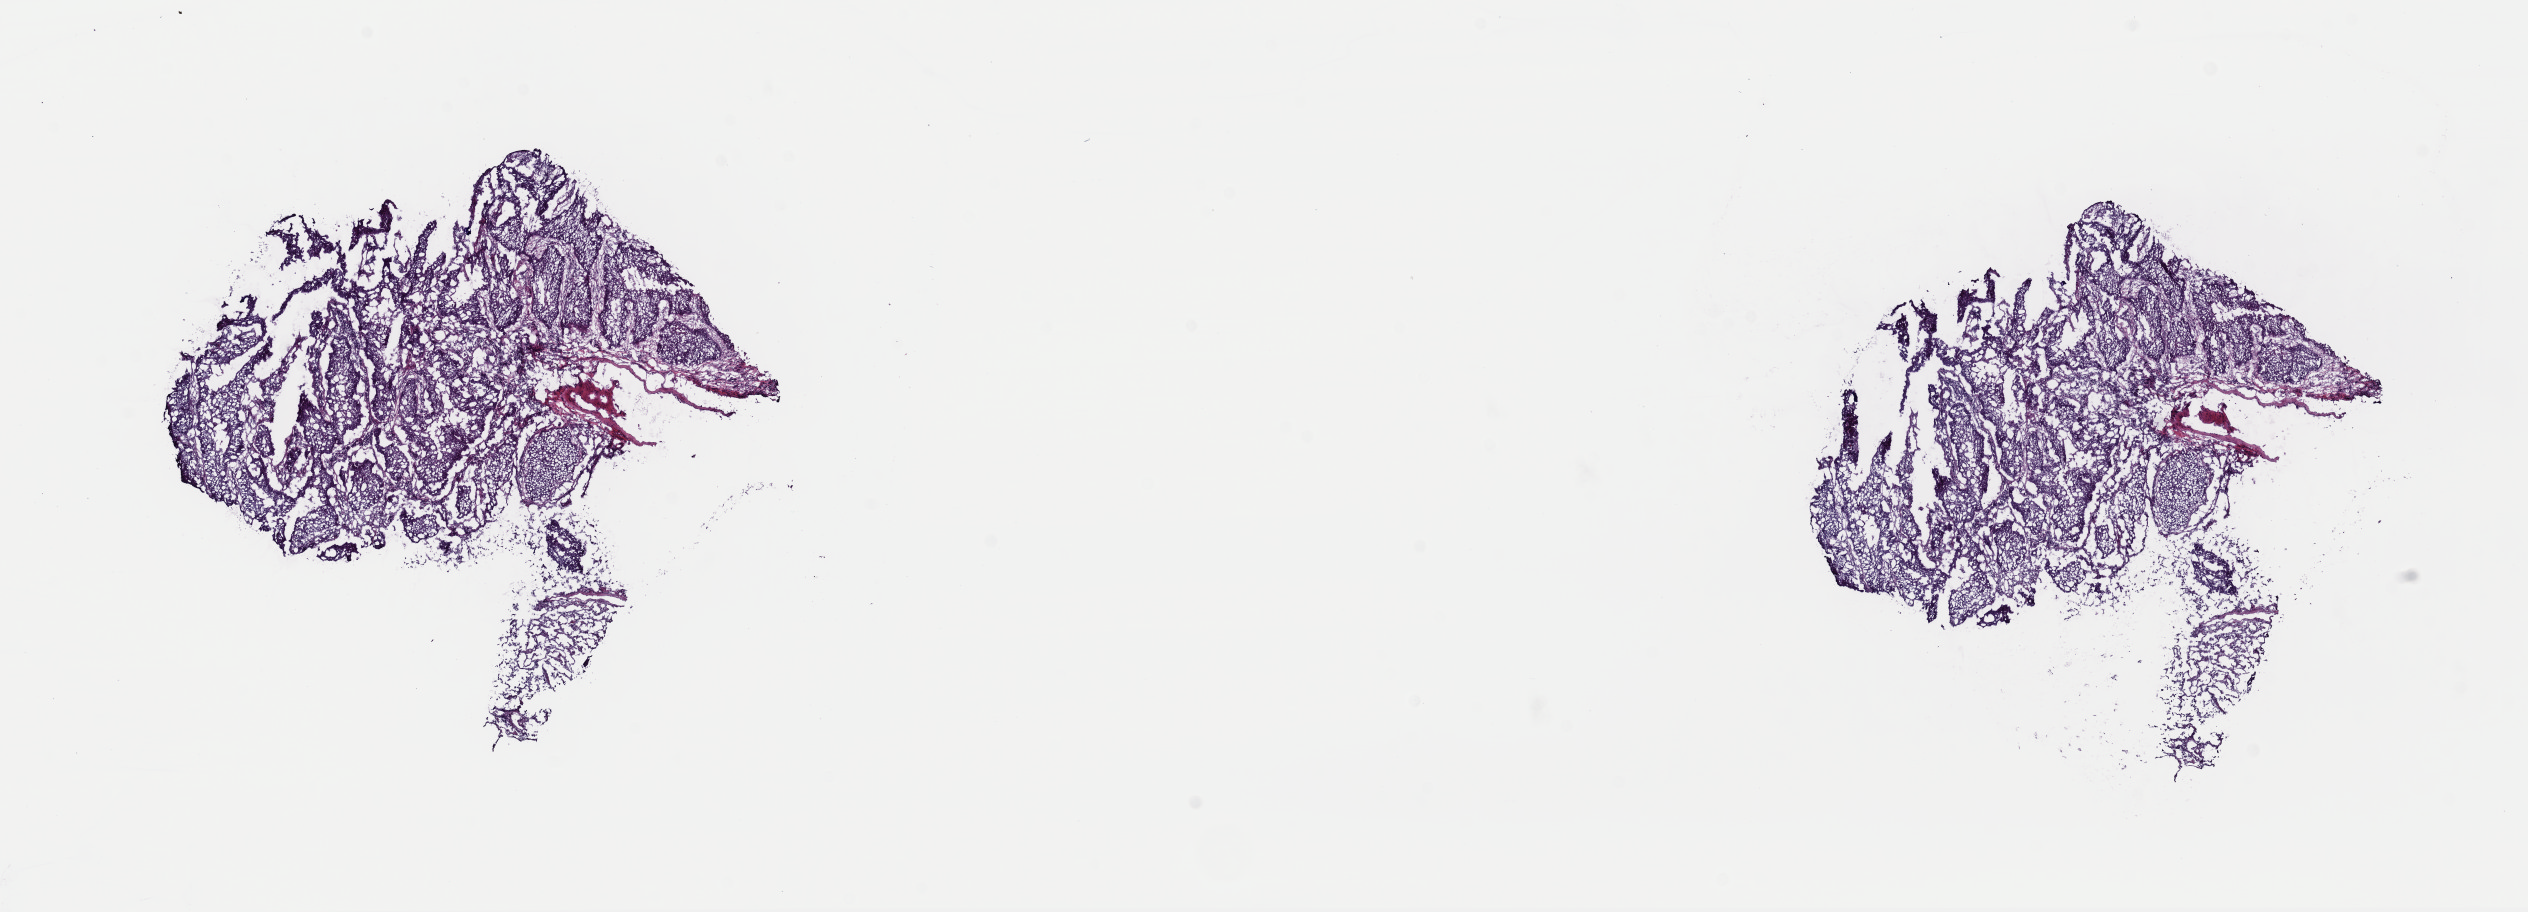
Hematoxylin and eosin (H&E) stained whole-slide image, low-resolution overview of the scanned area, about 20.0 x 7.2 mm (slide scanned at 40x), frozen section from the top of the tissue portion, lung, primary tumour sample. Male patient; age at initial diagnosis 70 years. Composition of this section per pathologist review: tumour cells 90%, tumour nuclei 100%, normal cells 0%, stromal cells 10%, necrosis 0%. Inflammatory infiltration, as recorded: lymphocyte infiltration 1%, monocyte infiltration 1%, neutrophil infiltration 0%.
AJCC pathologic stage: IB. Pathologic diagnosis: Squamous cell carcinoma, NOS (middle lobe, lung). Laterality: right.